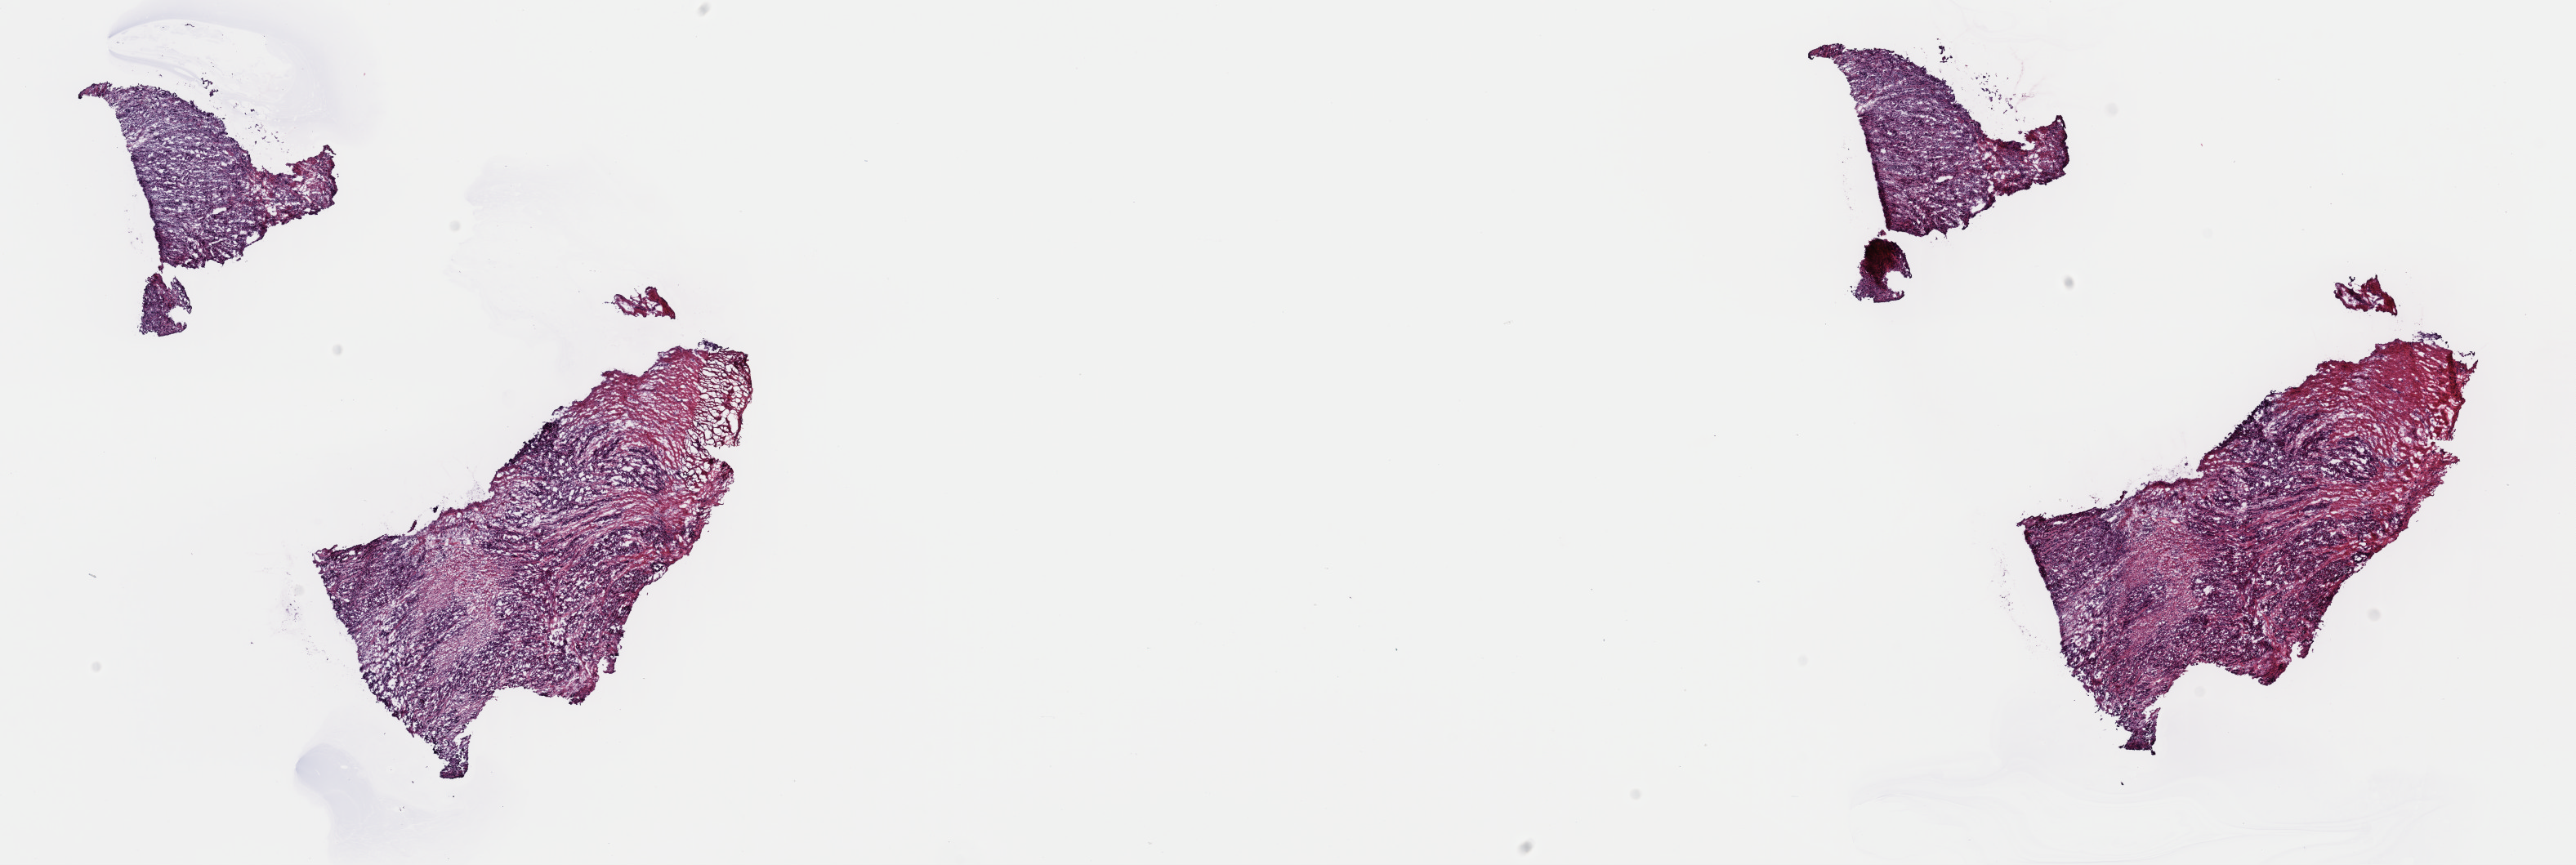
H&E-stained whole-slide image, a low-resolution overview of the entire scanned area, about 24.9 x 8.4 mm (slide scanned at 40x), frozen section, sample: primary tumour, stomach. Female patient; age at initial diagnosis 70 years. Histologic grade: G3 (poorly differentiated). Slide review estimates, as recorded: tumour cells 100%, tumour nuclei 75%, normal cells 0%, stromal cells 0%, necrosis 0%. Infiltration values recorded for this section: lymphocyte infiltration 2%, monocyte infiltration 0%, neutrophil infiltration 0%.
AJCC pathologic stage: IIA. Diagnosis: Adenocarcinoma, NOS.